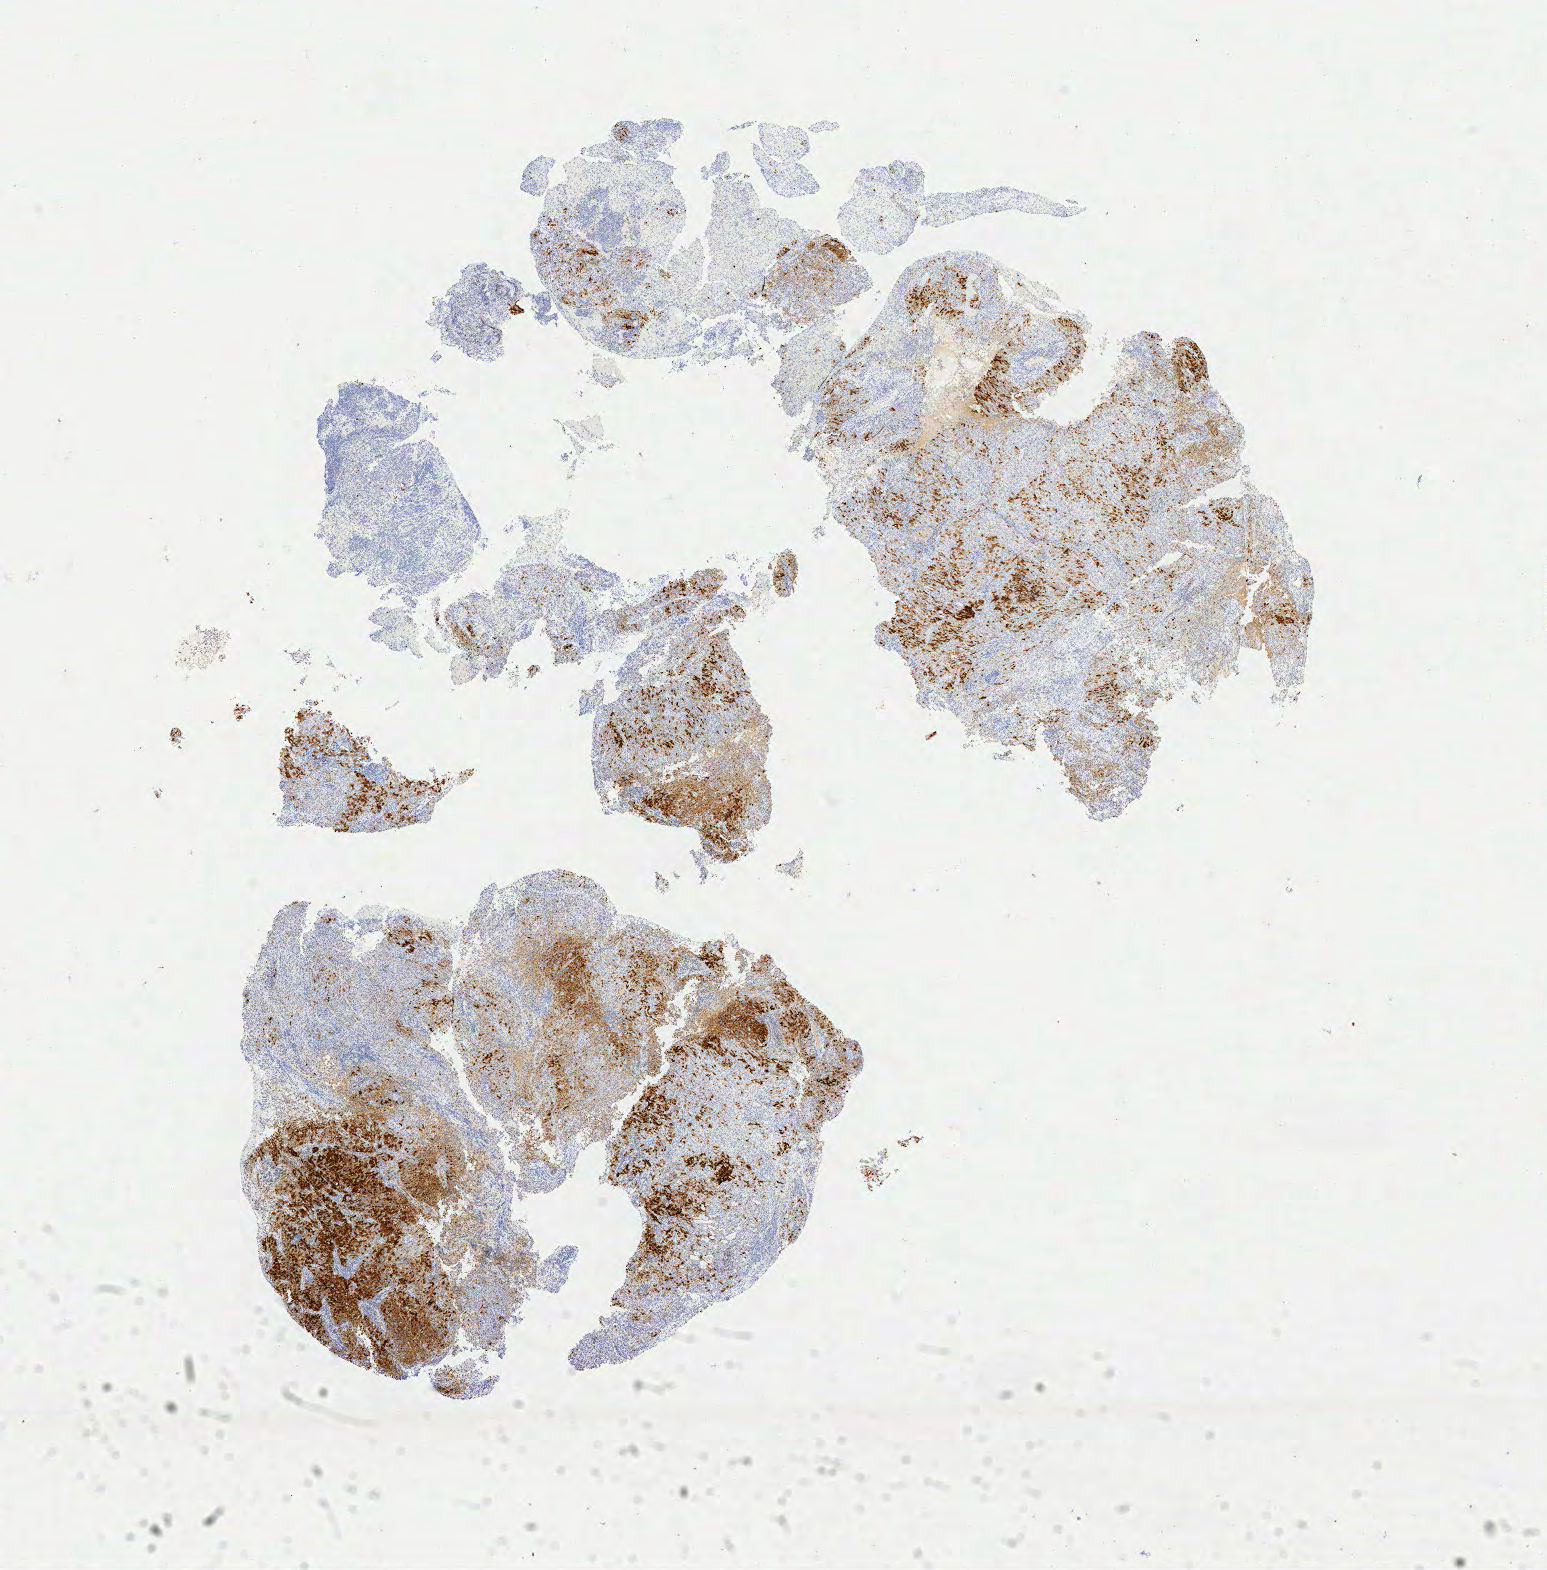
Immunohistochemistry (IHC) whole-slide image stained for p16 (p16INK4a), whole scanned area (about 12.3 x 12.5 mm) shown as a low-resolution overview. Tumor tissue. Anatomic site: cervix. Female patient, aged 70.
Diagnosis: Squamous cell carcinoma, large cell, nonkeratinizing, NOS.